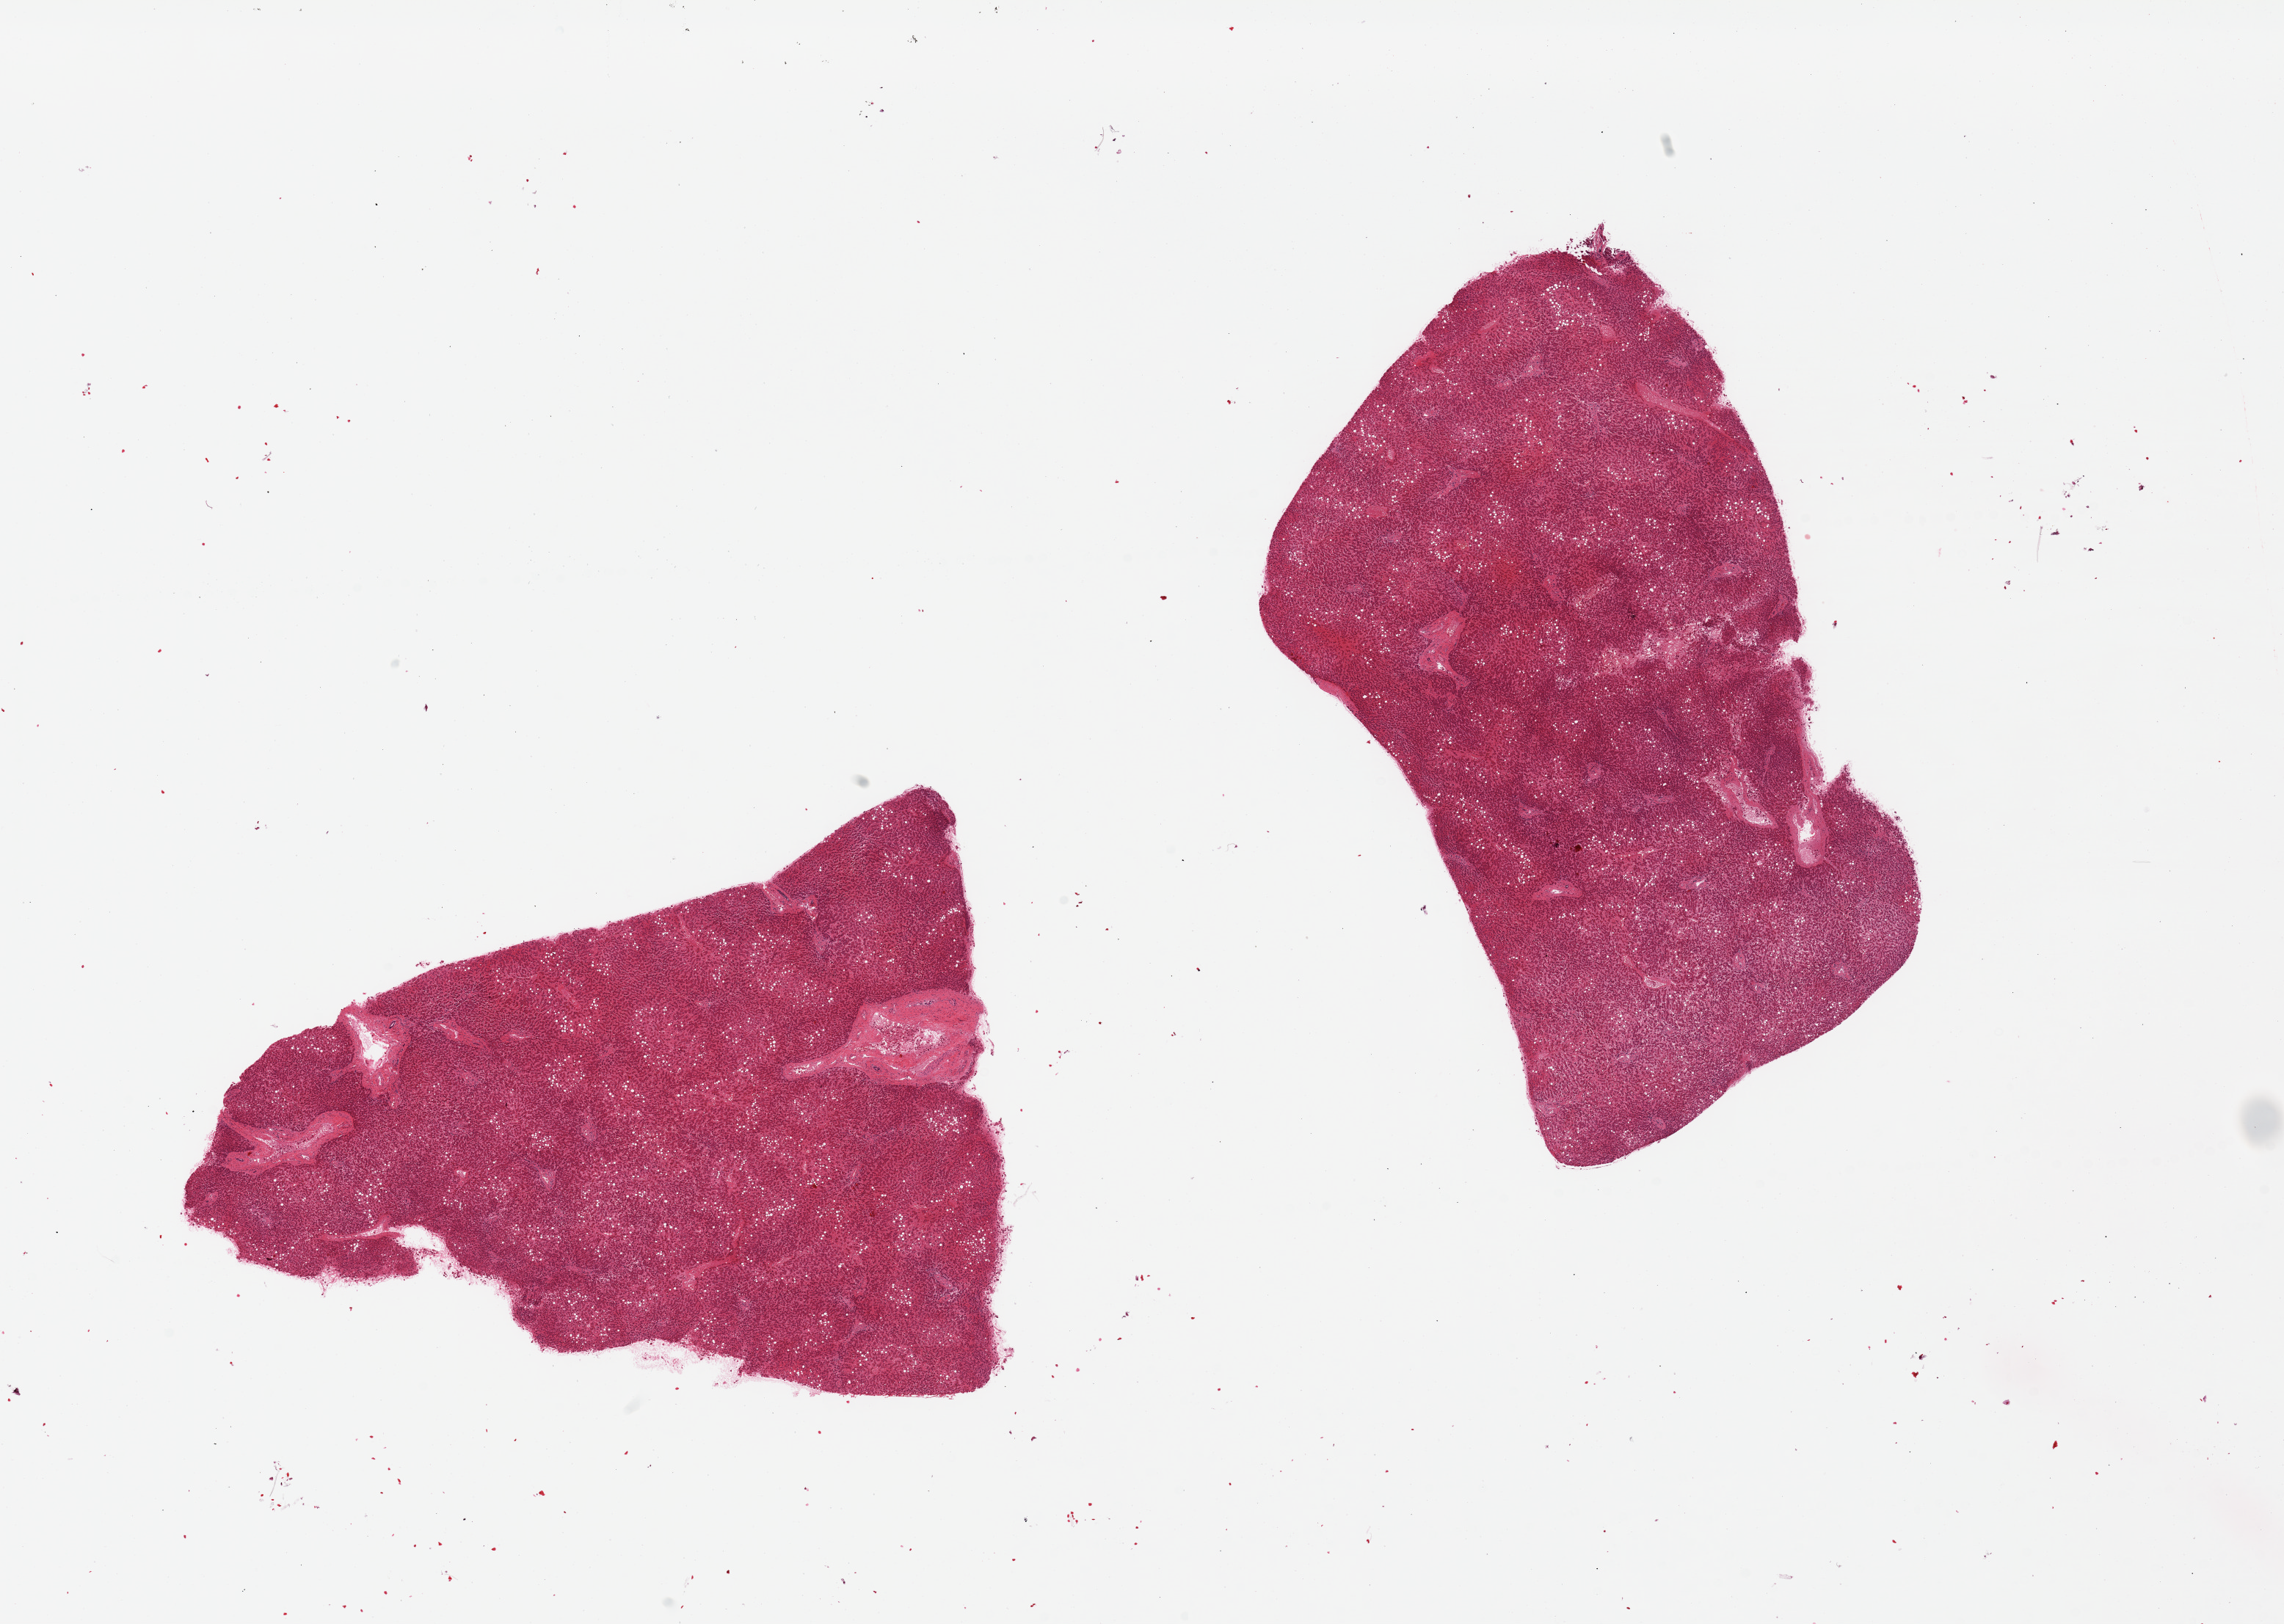
Haematoxylin and eosin whole-slide image, a low-resolution overview of the entire scanned area, about 24.6 x 17.5 mm. PAXgene-fixed paraffin-embedded (PFPE) section. Section of liver (target tissue). Tissue donor sample. Male donor.
- pathologist's review note for this sample: 2 pieces. moderate vascular congestion.. 10% macrovesicular steatosis